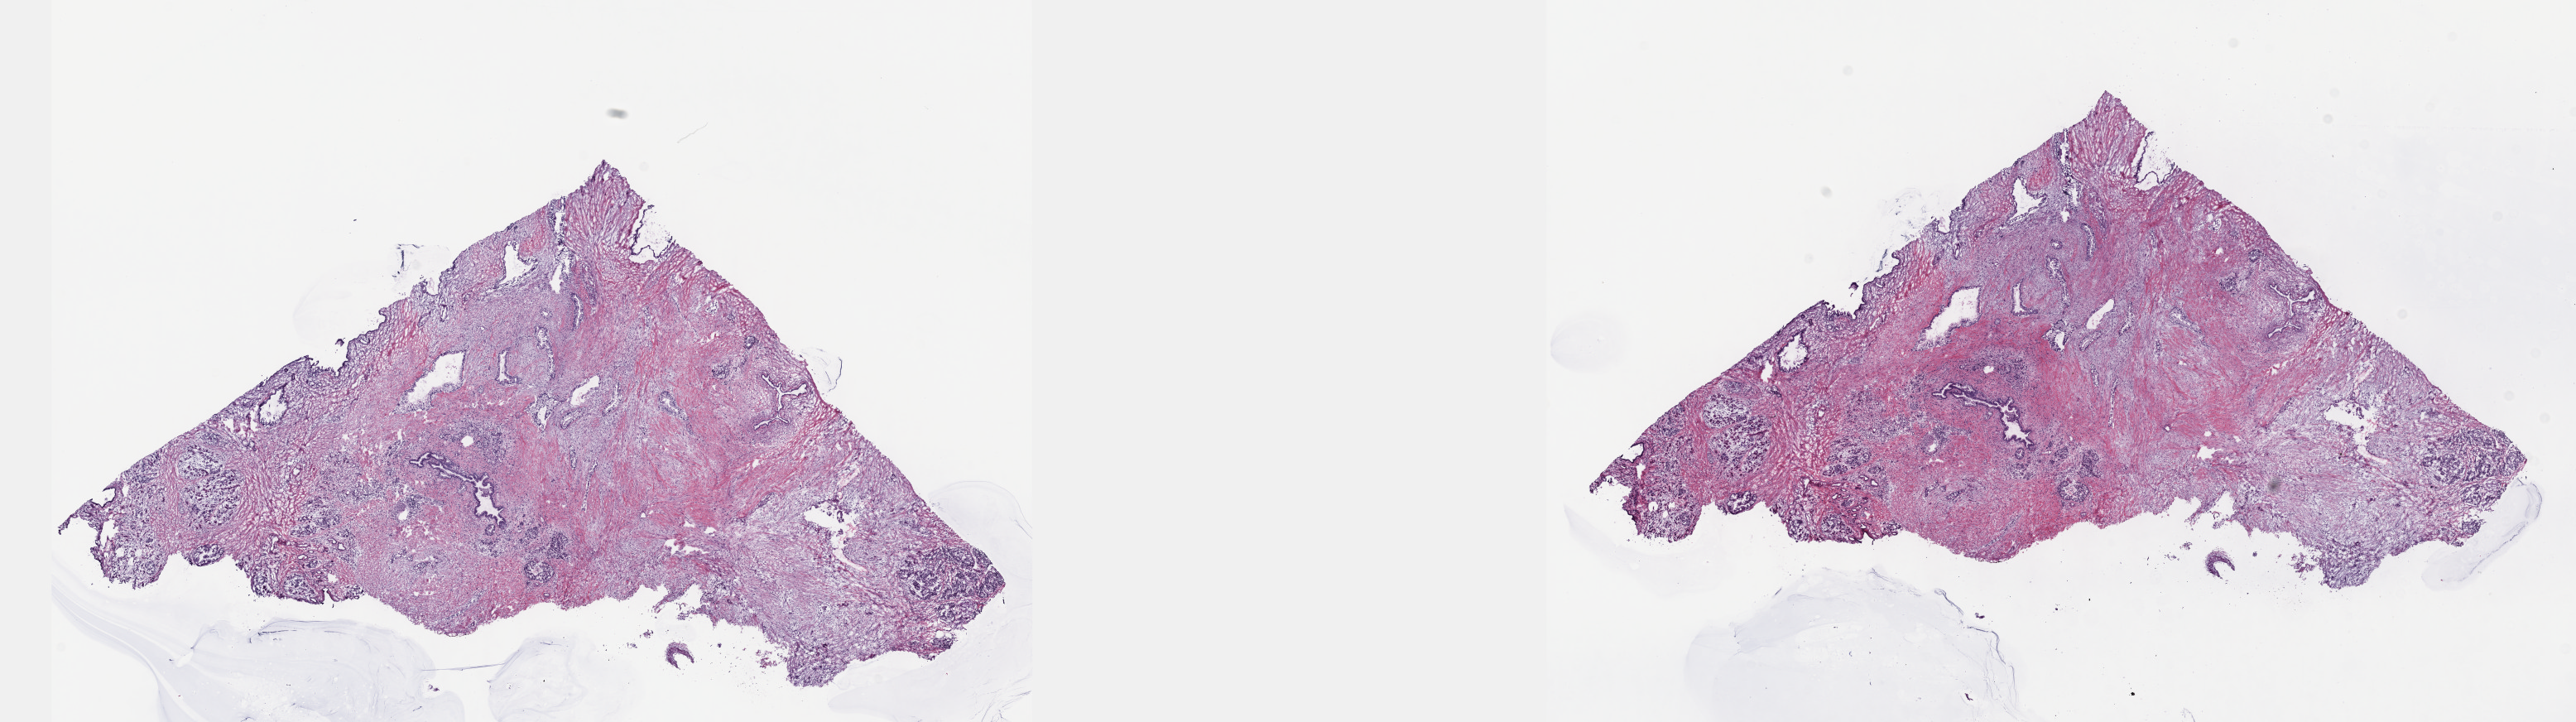
Hematoxylin and eosin (H&E) stained whole-slide image — shown as a low-resolution overview of the whole scanned area (about 25.1 x 7.0 mm), frozen section from the top of the tissue portion, pancreas, primary tumour sample. Female patient; age at initial diagnosis 66 years. Histologic grade: G2 (moderately differentiated). Composition of this section per pathologist review: tumour cells 50%, tumour nuclei 50%, normal cells 20%, stromal cells 30%, necrosis 0%. Infiltration values recorded for this section: lymphocyte infiltration 70%, monocyte infiltration 10%, neutrophil infiltration 10%.
• AJCC pathologic stage: IV
• diagnosis: Infiltrating duct carcinoma, NOS (body of pancreas)
• lymph nodes positive (case pathology): 1 of 12 examined